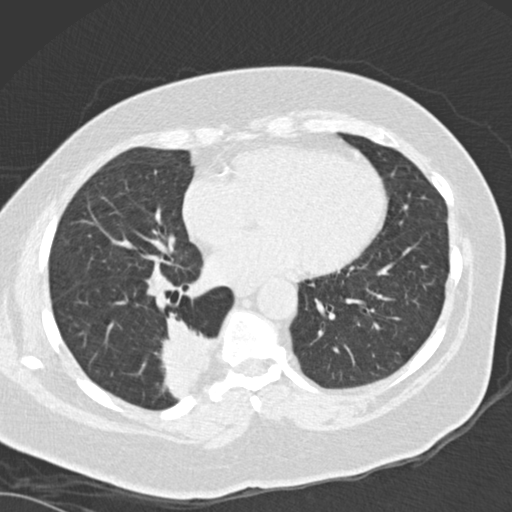
Low-dose screening chest CT, one axial slice. Position 65 of 162 along the scan axis. Reconstruction kernel B30f. 120 kVp. Lung window (W 1500 / L -600 HU). 2 mm slice thickness. 512 × 512 image matrix.
Structures marked on this image (expert manual segmentation):
- lesion 1 (tumor, lower lobe of right lung): box from (x=160, y=312) to (x=215, y=401) px